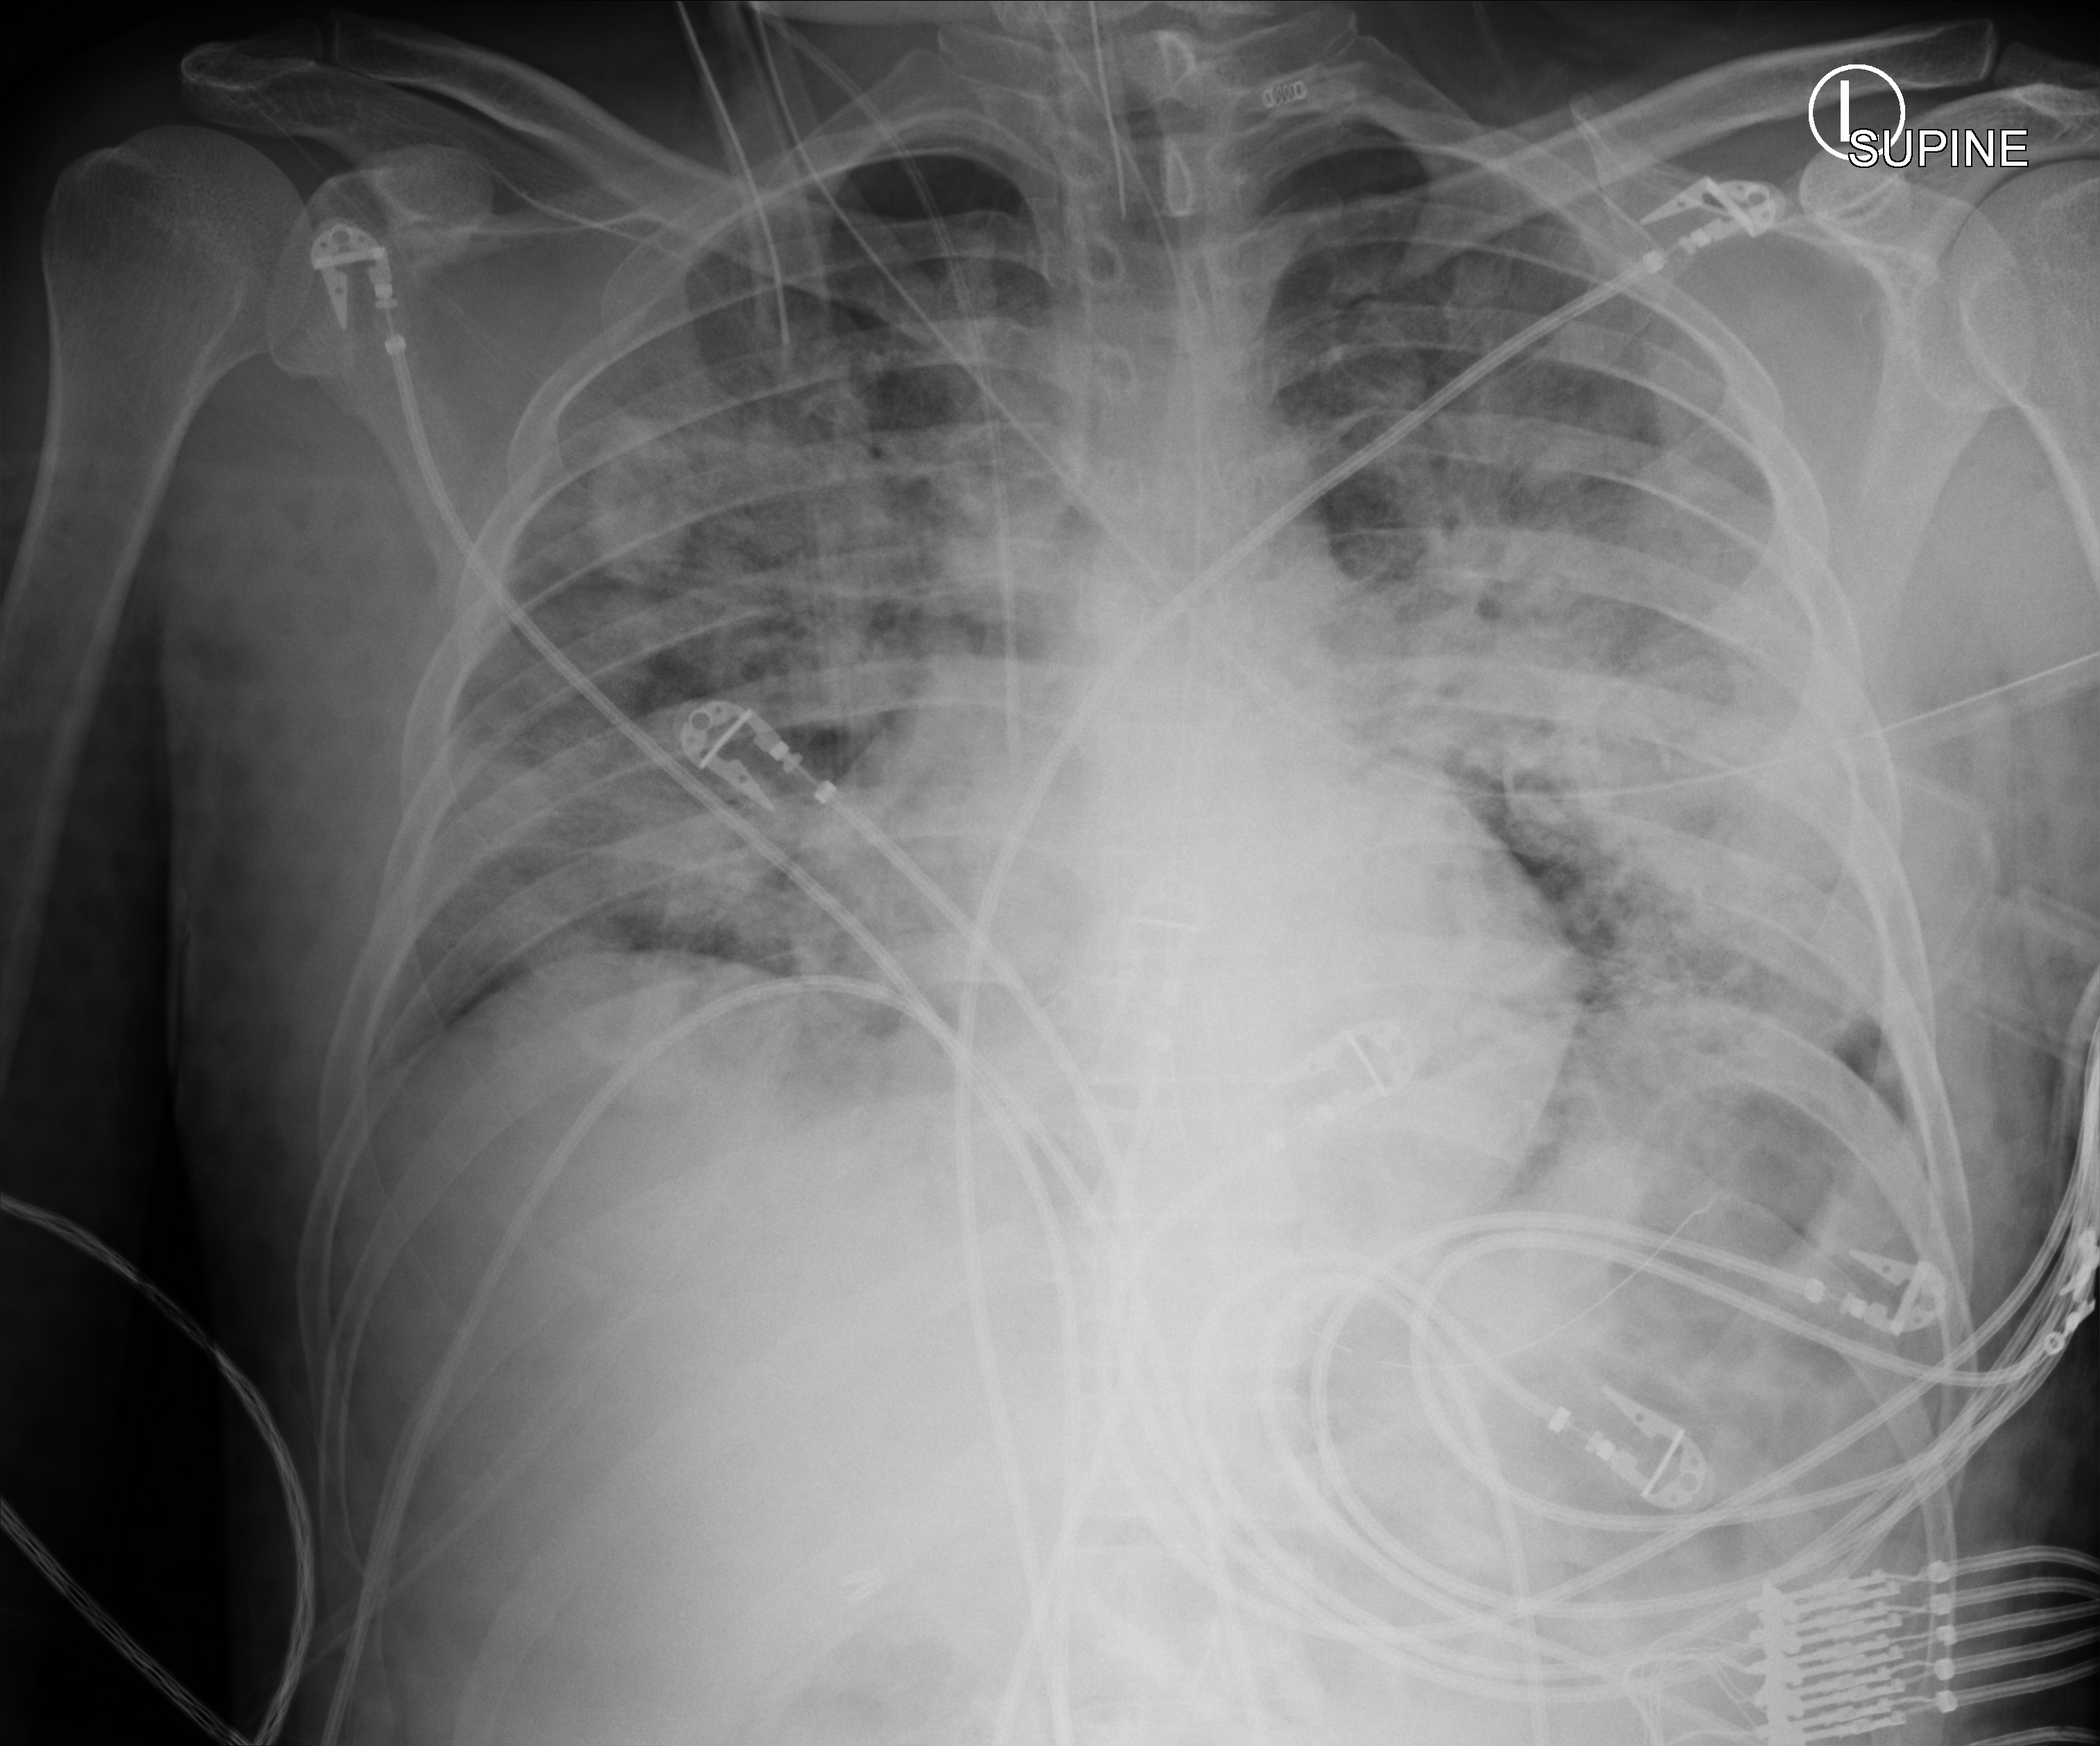
Chest X-ray (portable); anteroposterior (AP) projection. Patient hospitalised with COVID-19; male, aged 18–59 years.
From the hospital-stay record, not from the radiograph (when in the stay this image was taken is not recorded):
- admitted to intensive care during this hospital stay: yes
- mechanically ventilated during this hospital stay: yes